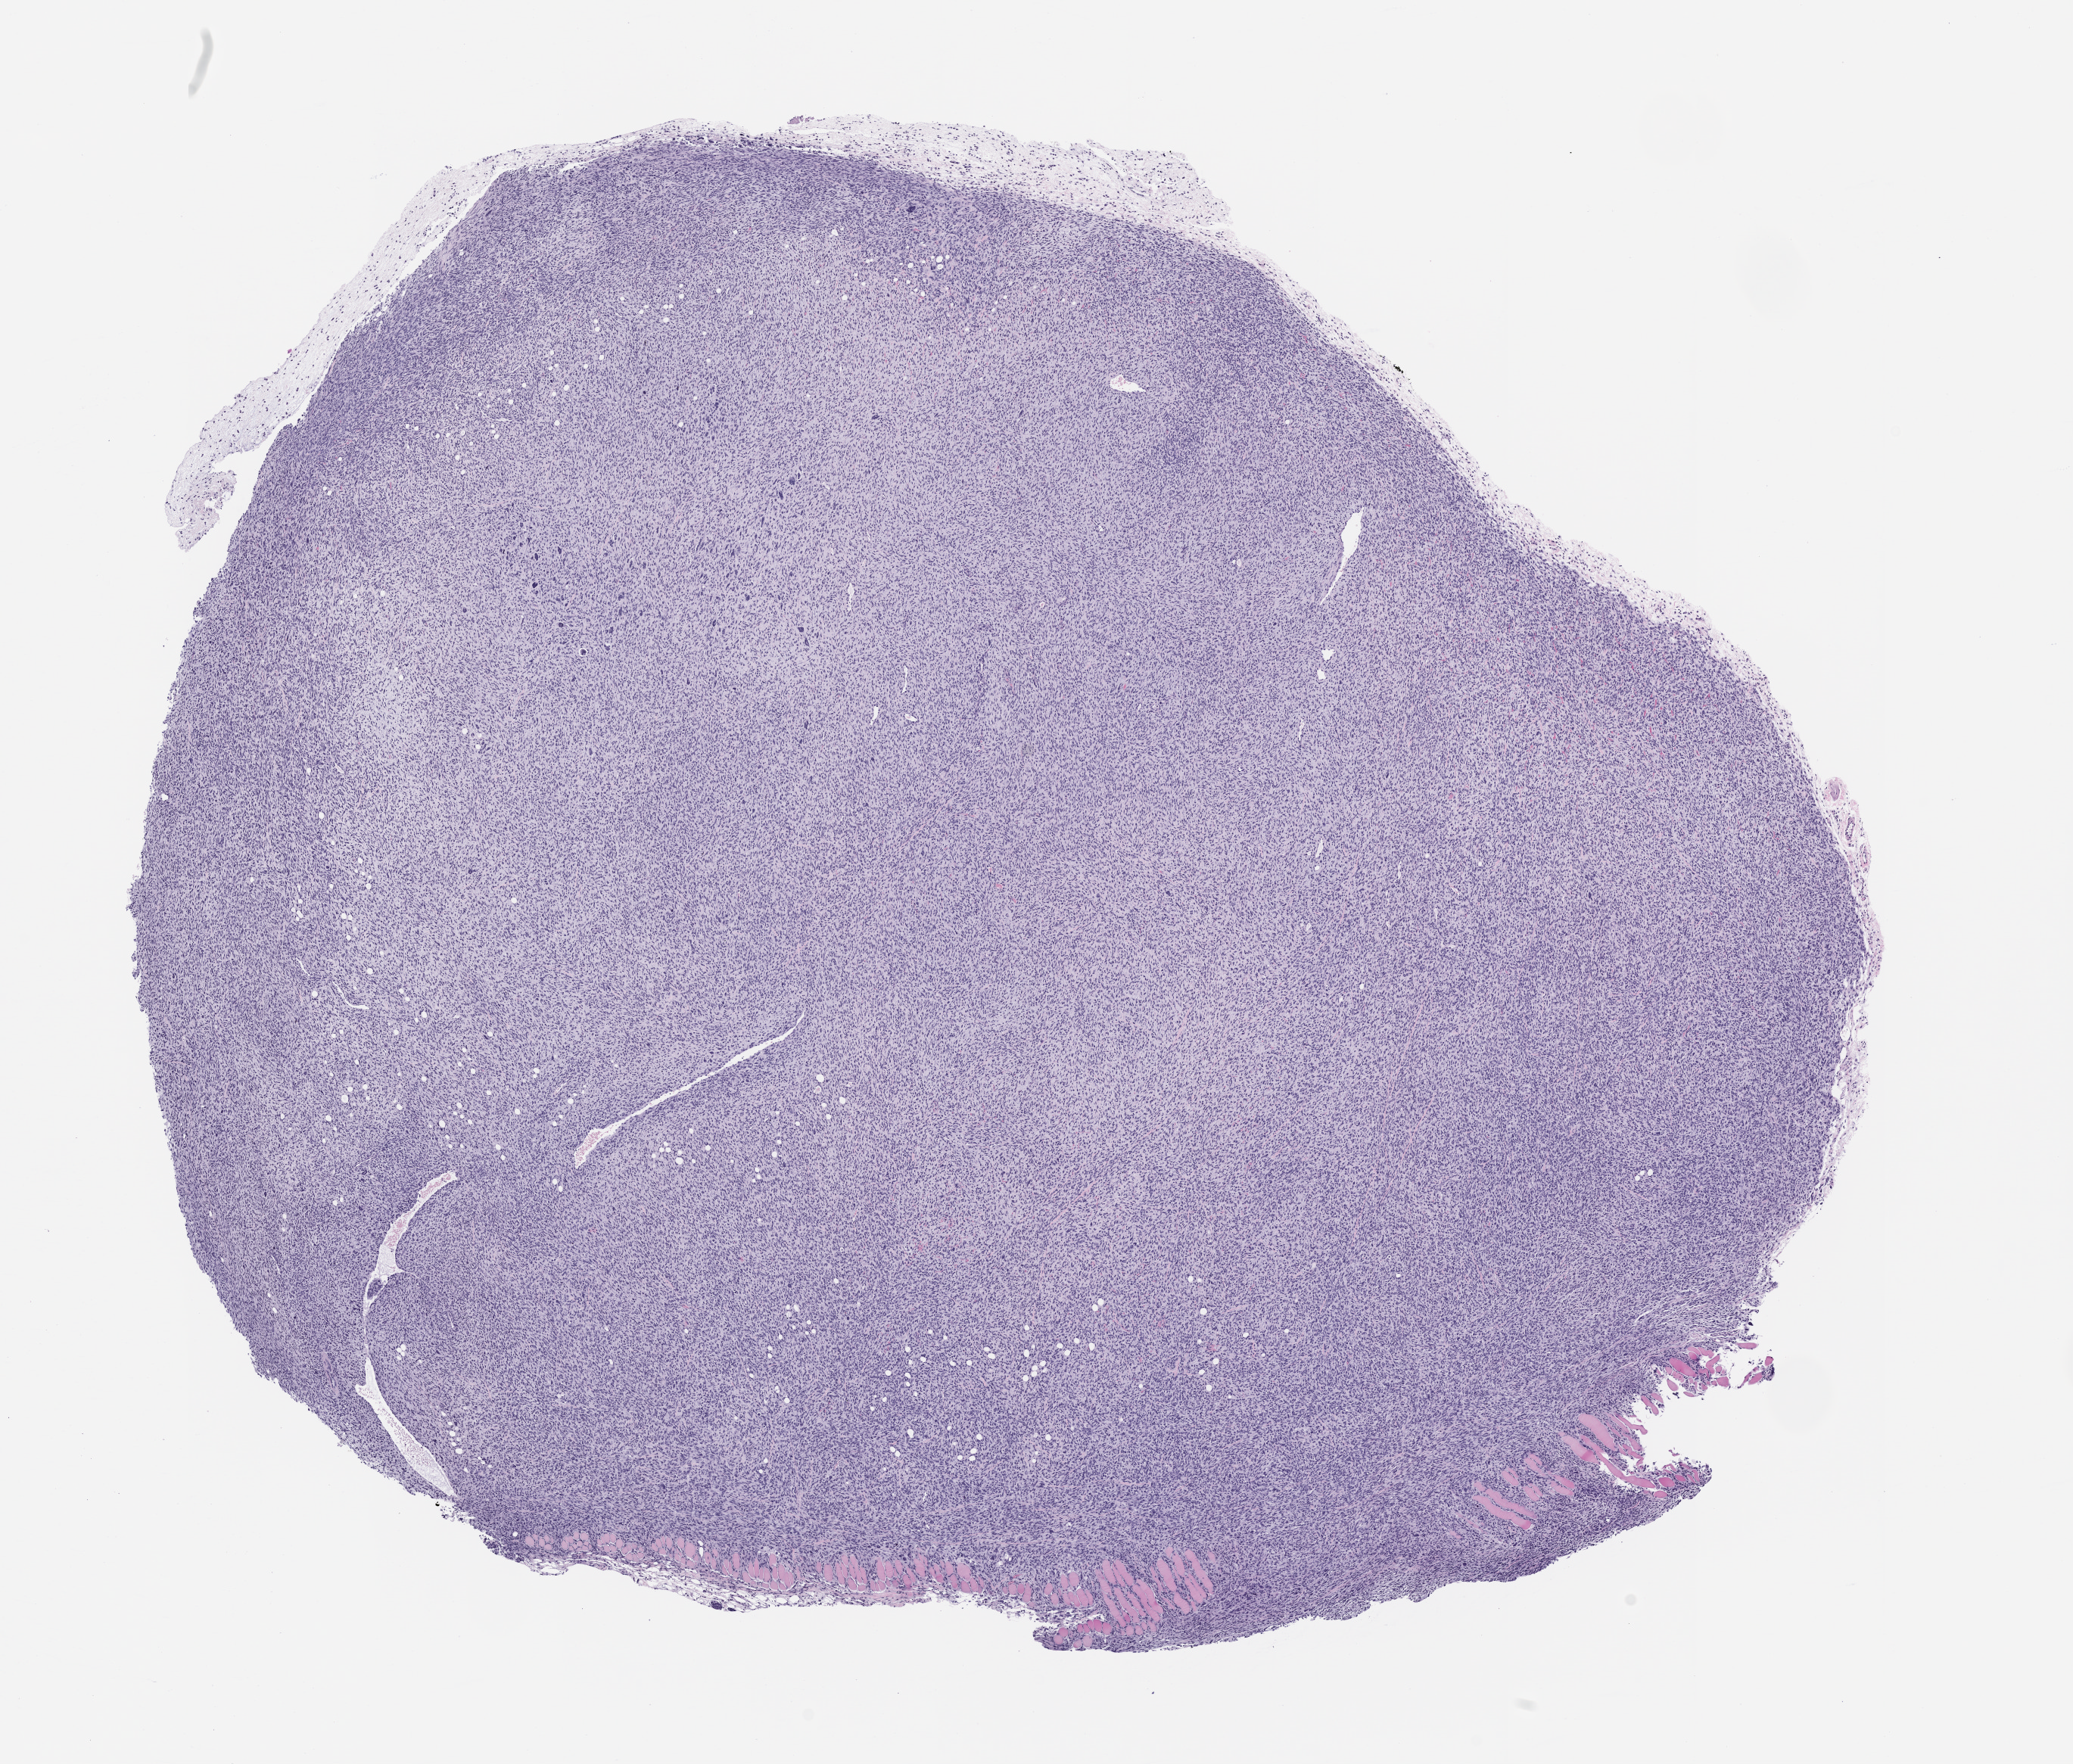
Whole-slide image, H&E: patient-derived xenograft (human tumor grown in a mouse), passage 0, shown as a low-resolution overview of the whole scanned area (about 11.0 x 9.4 mm), formalin-fixed paraffin-embedded section, tumor site category: peripheral nervous system.
Originating patient diagnosis: Malignant Peripheral Nerve Sheath Tumor.